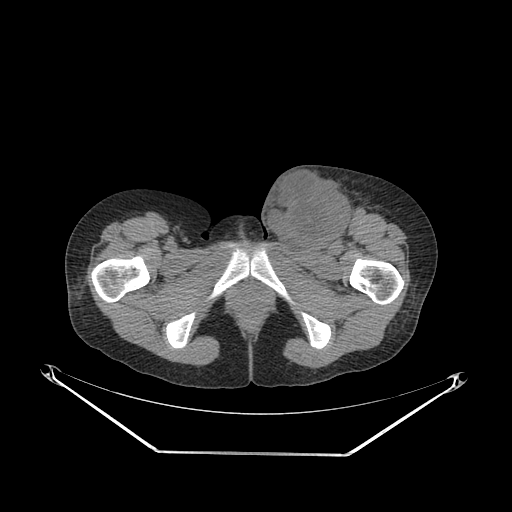
CT of an extremity soft-tissue mass (from a PET/CT study), one axial slice; slice 58 of 267 in the series (ordered by position); 140 kVp; soft-tissue window (W 400 / L 40 HU); 512 × 512 image matrix. Female patient. From the clinical record (not read from this slice): histological type: leiomyosarcoma; grade: high; site of the primary tumour: groin.
Outlined on this slice (expert contour drawn on MRI and transferred to this co-registered scan by the dataset authors):
- gross tumour volume including surrounding oedema: box from (x=258, y=165) to (x=369, y=252) px
- gross tumour volume (mass): (x=263, y=171)–(x=350, y=248)